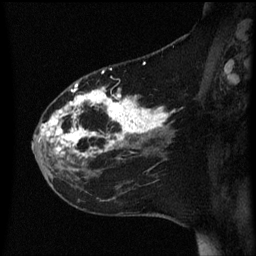
Breast MRI (dynamic contrast-enhanced), one sagittal slice. Position 21 of 60 along the scan axis. Dynamic contrast-enhanced series, image 2 of 3 at this slice position (ordered by acquisition). 1.5 T. TE 4.2 ms, TR 8.4 ms. 2.2 mm slice thickness. 256 × 256 image matrix, field of view 200 × 200 mm. Patient: female, 35 years. Case-level facts recorded for this patient, not image findings: setting: breast cancer imaged before/during neoadjuvant chemotherapy; receptor status: HER2-positive.
Structures marked on this image (semi-automatically segmented with operator editing):
- analysis volume of interest (the breast-tissue region the enhancement analysis was run in; not a lesion): bounding box [x1, y1, x2, y2] px = [33, 78, 173, 163]
- tumour enhancement mask (voxels above the 70 % enhancement threshold inside the analysis volume of interest): [42, 84, 169, 157]